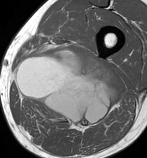
MRI of an extremity soft-tissue mass, one axial slice; slice 52 of 86 in the series (ordered by position); MR volume resampled by the dataset authors to the PET/CT grid (not the native acquisition matrix); 3.27 mm slice thickness; 147 × 158 image matrix, field of view 144 × 154 mm. Male patient. From the clinical record (not read from this slice): histological type: undifferentiated pleomorphic liposarcoma; grade: high; site of the primary tumour: left thigh.
Annotated regions visible in this slice (expert contour drawn on MRI and transferred to this co-registered scan by the dataset authors):
- gross tumour volume including surrounding oedema: bounding box <16,47,120,130> (left, top, right, bottom; pixels)
- gross tumour volume (mass): <16,47,120,128>